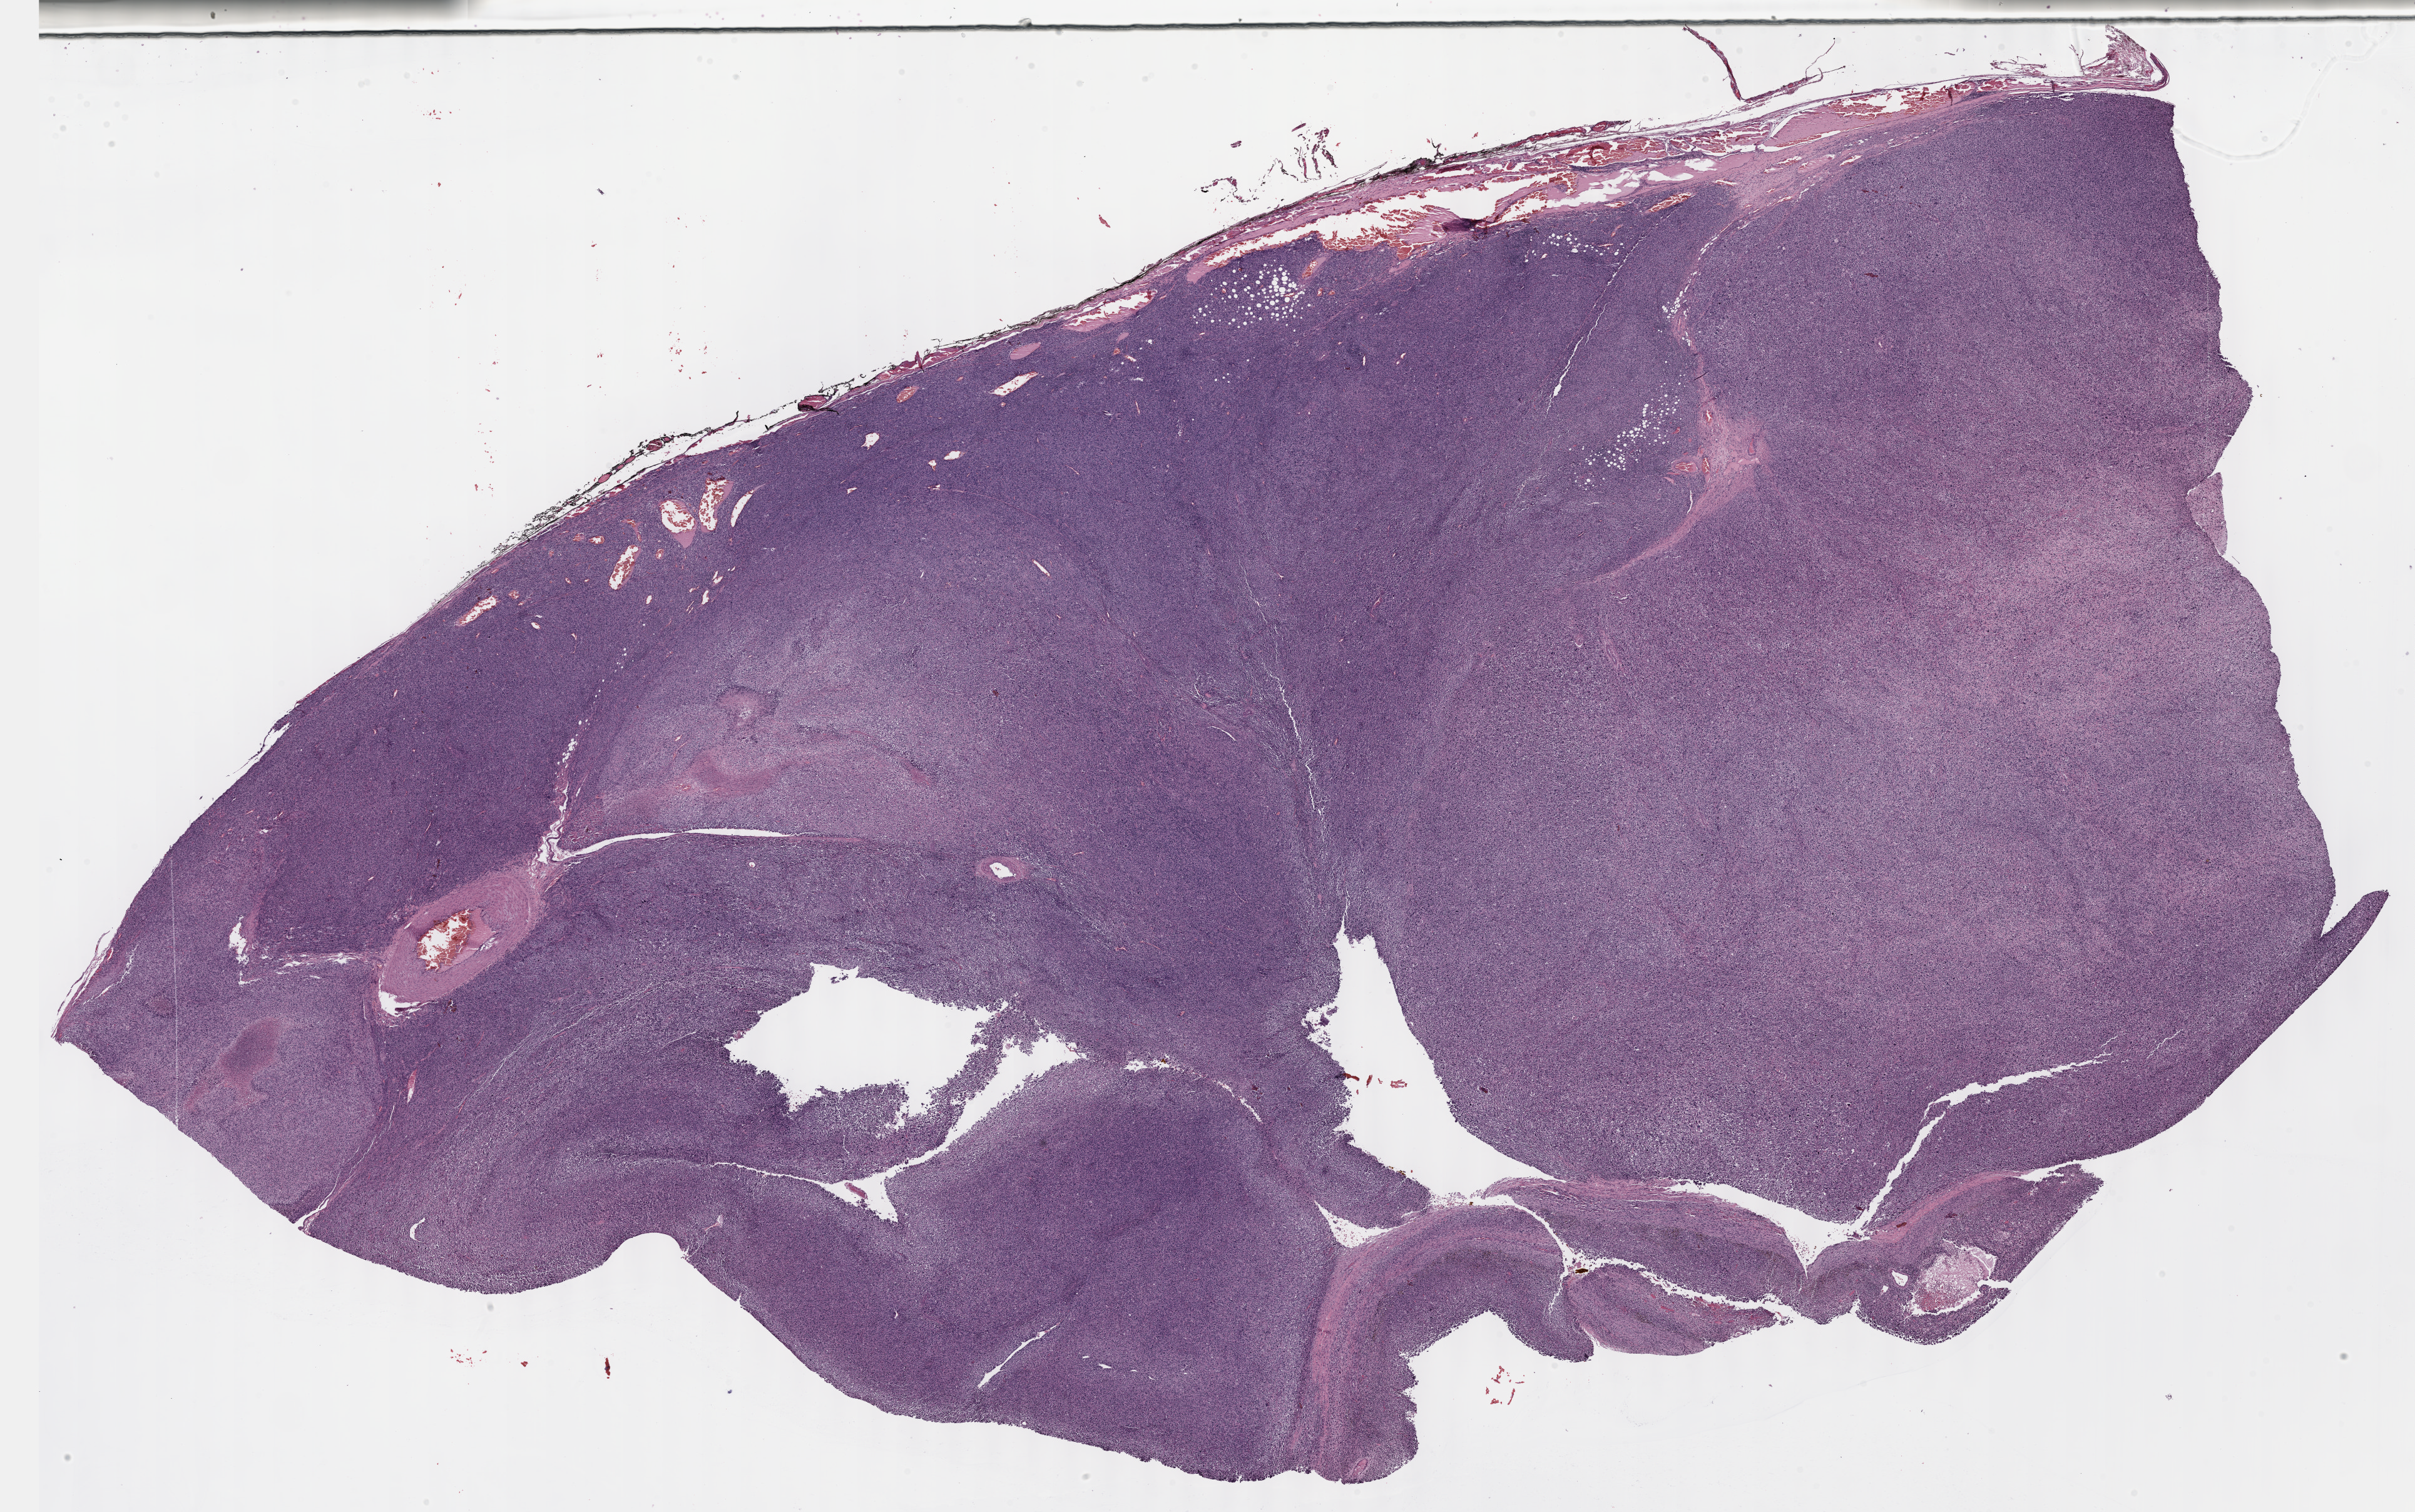
Whole-slide histology image, Hematoxylin and eosin (H&E) stained — a low-resolution overview of the entire scanned area, about 31.2 x 19.5 mm (from a 40x scan), formalin-fixed paraffin-embedded (FFPE) diagnostic section, connective, subcutaneous and other soft tissues, primary tumour sample. Male, age 29 years at initial diagnosis.
- histologic diagnosis: Malignant peripheral nerve sheath tumor (connective, subcutaneous and other soft tissues of lower limb and hip)